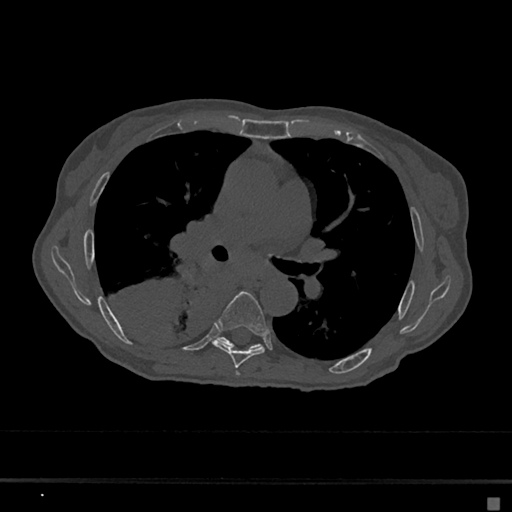
CT including the spine, one axial slice; position 406 of 797 along the scan axis; bone window (W 1800 / L 400 HU); 512 × 512 image matrix, field of view 360 × 360 mm. Patient: female, 68 years. Case-level facts recorded for this patient, not image findings: primary cancer: renal.
Annotated regions visible in this slice (semi-automatically segmented with operator editing):
- T5 vertebra: bounding box [x1, y1, x2, y2] px = [236, 371, 240, 376]
- T6 vertebra: [213, 291, 269, 368]
- T7 vertebra: [218, 337, 261, 348]